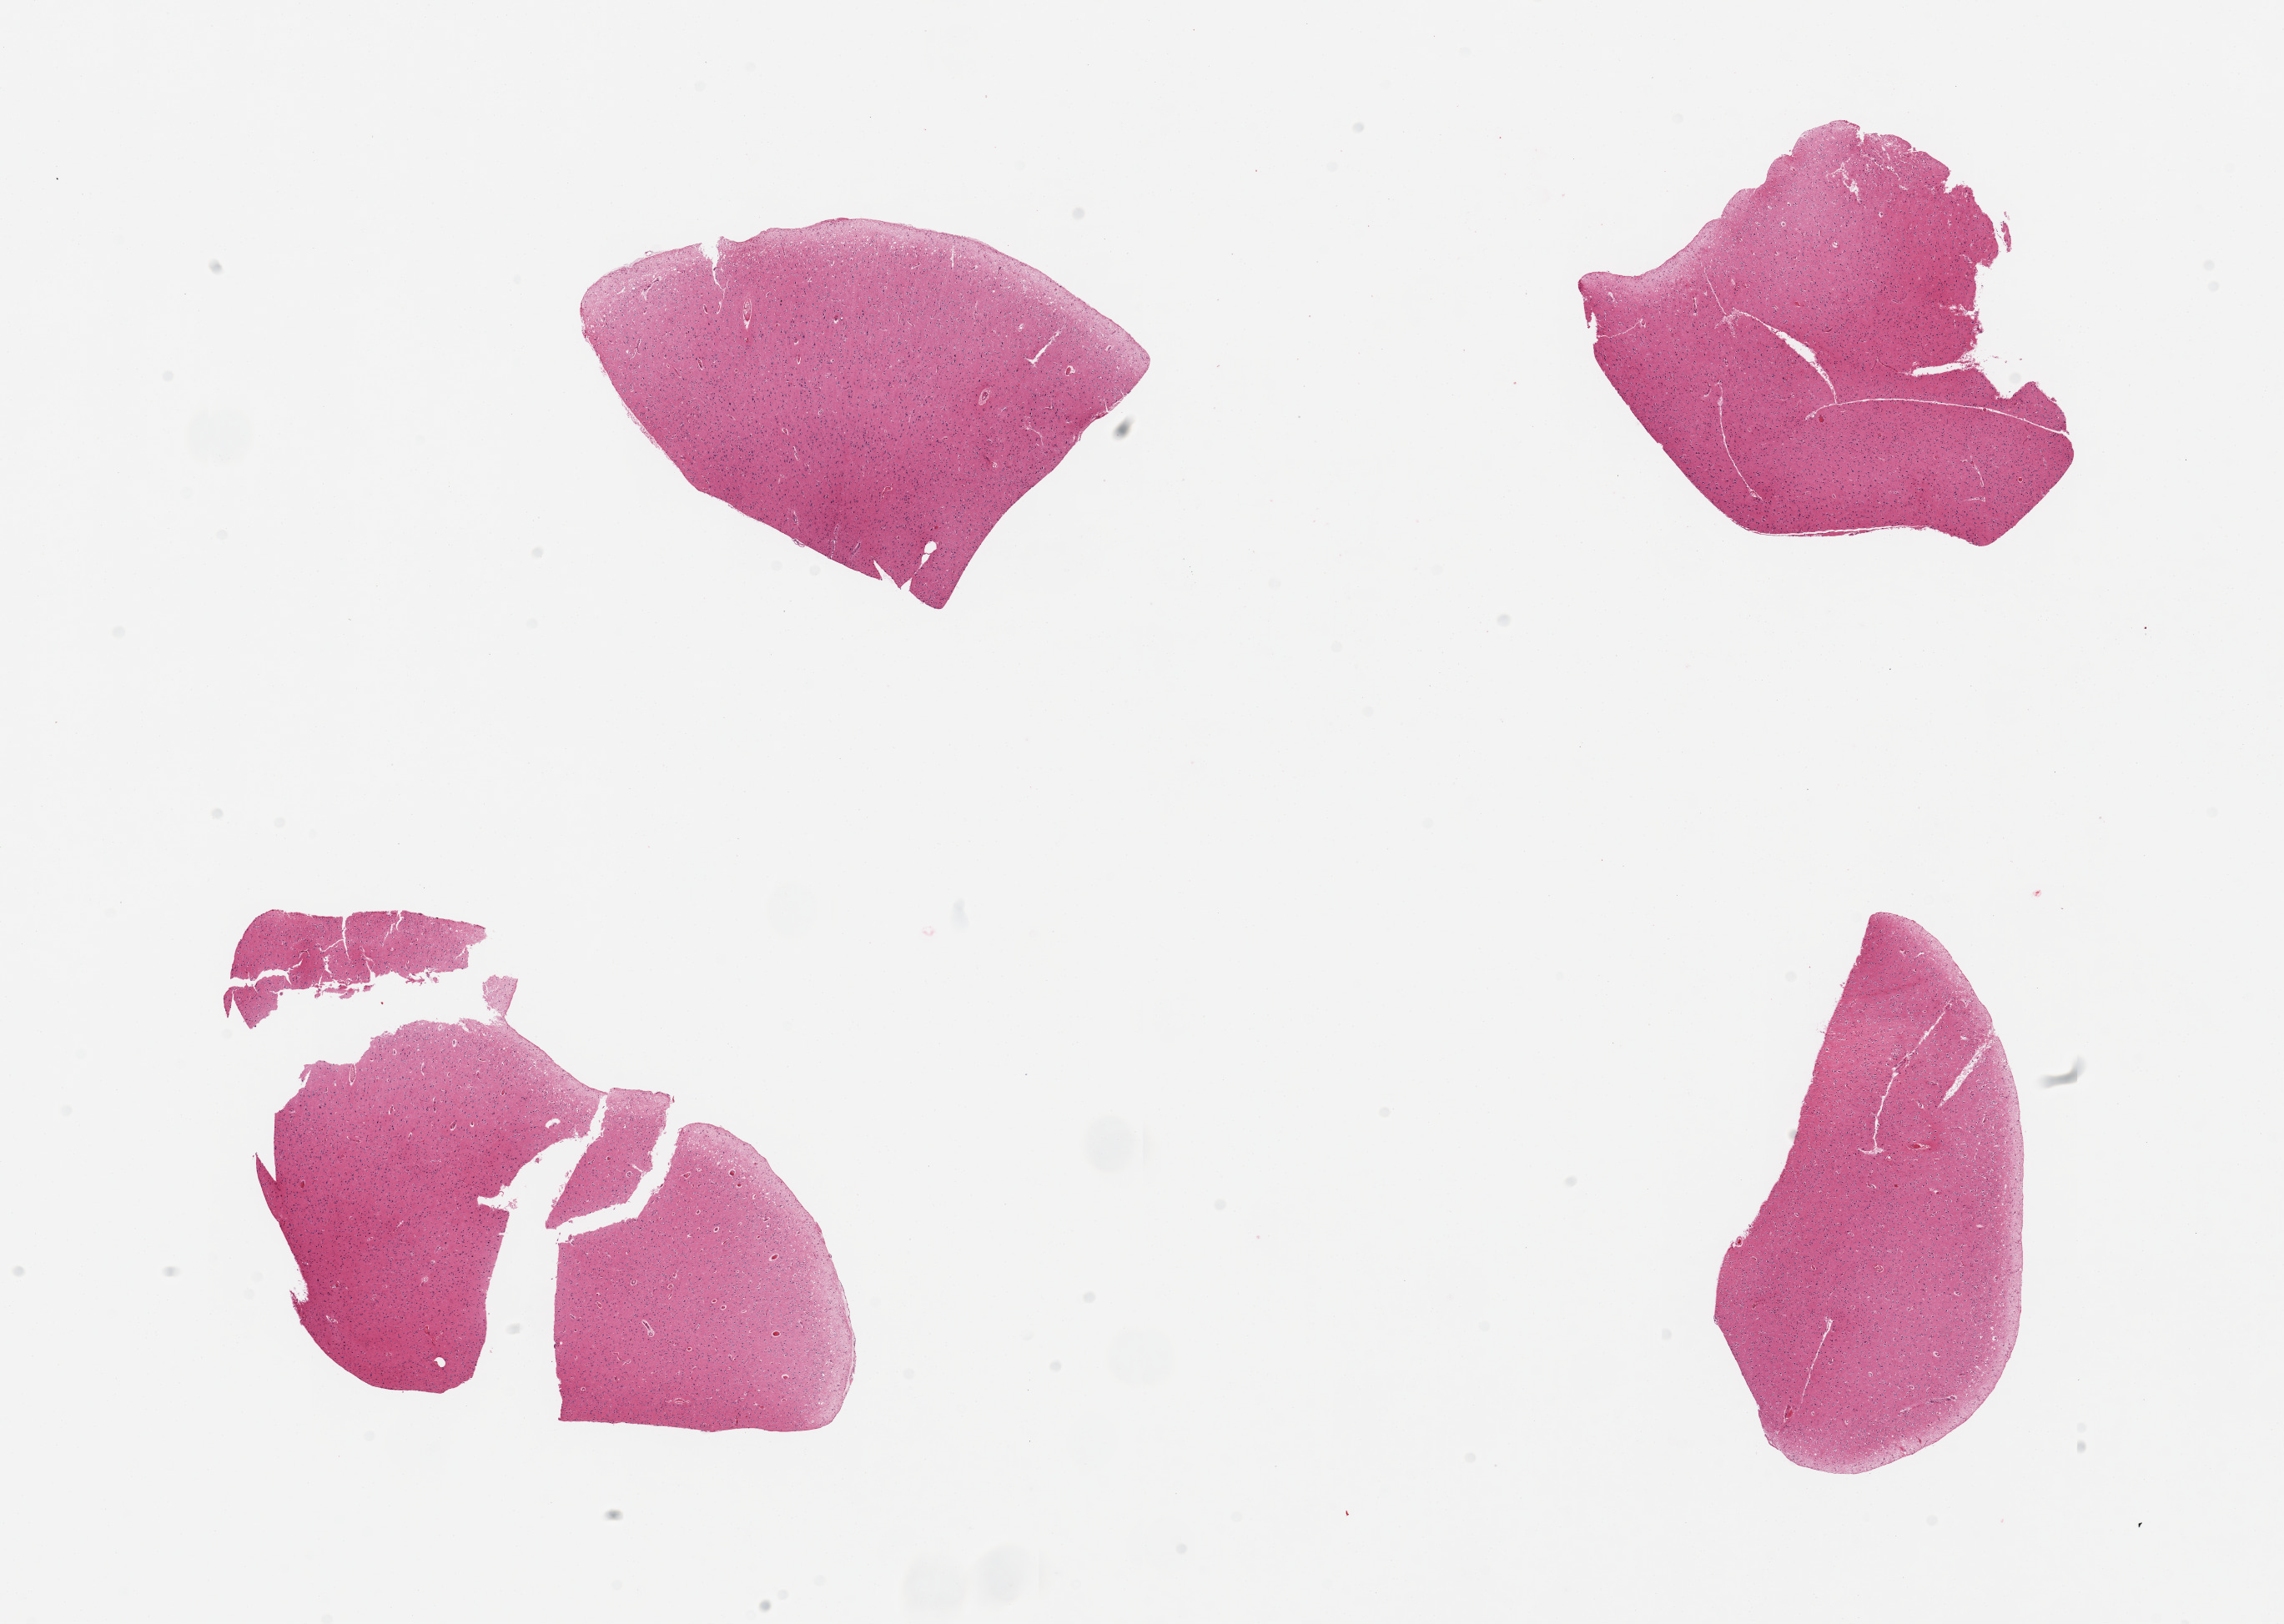
Hematoxylin and eosin (H&E) whole-slide image — a low-resolution overview of the entire scanned area, about 21.7 x 15.4 mm (acquisition: 20x scan). PAXgene-fixed paraffin-embedded (PFPE) section. Section of cerebral cortex (target tissue). Tissue donor sample. Donor: male.
Reviewer comment on this tissue sample: 4 pieces.